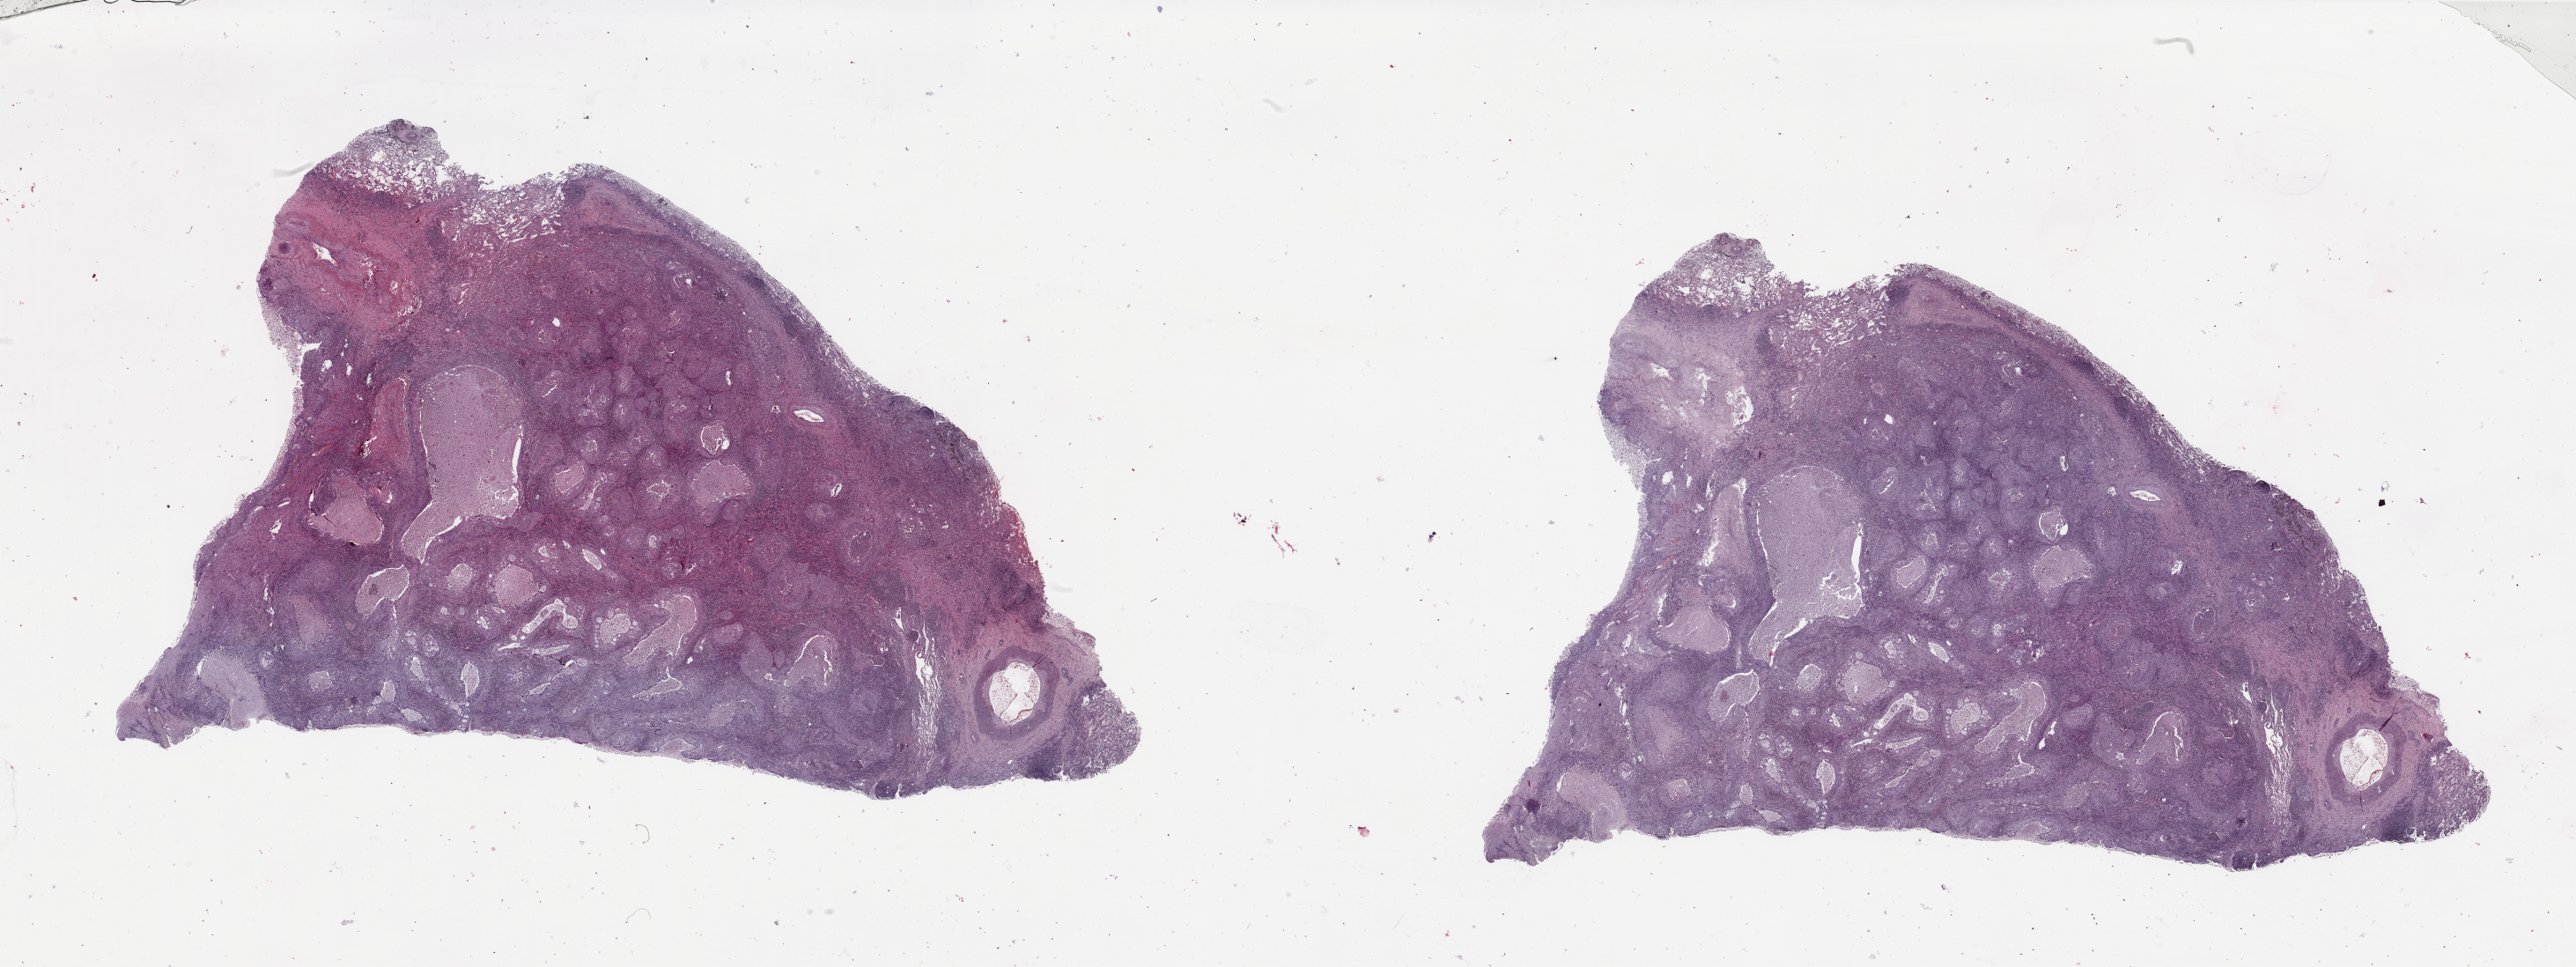
Whole-slide histology image, H&E — whole scanned area (about 46.3 x 17.4 mm) shown as a low-resolution overview. Tumour tissue sample, lung. Patient: male, age 70 years. Histologic grade: G2 (moderately differentiated).
AJCC pathologic stage: IB. Diagnosis: Squamous cell carcinoma, NOS. Primary tumour site (as recorded): left lower lobe.